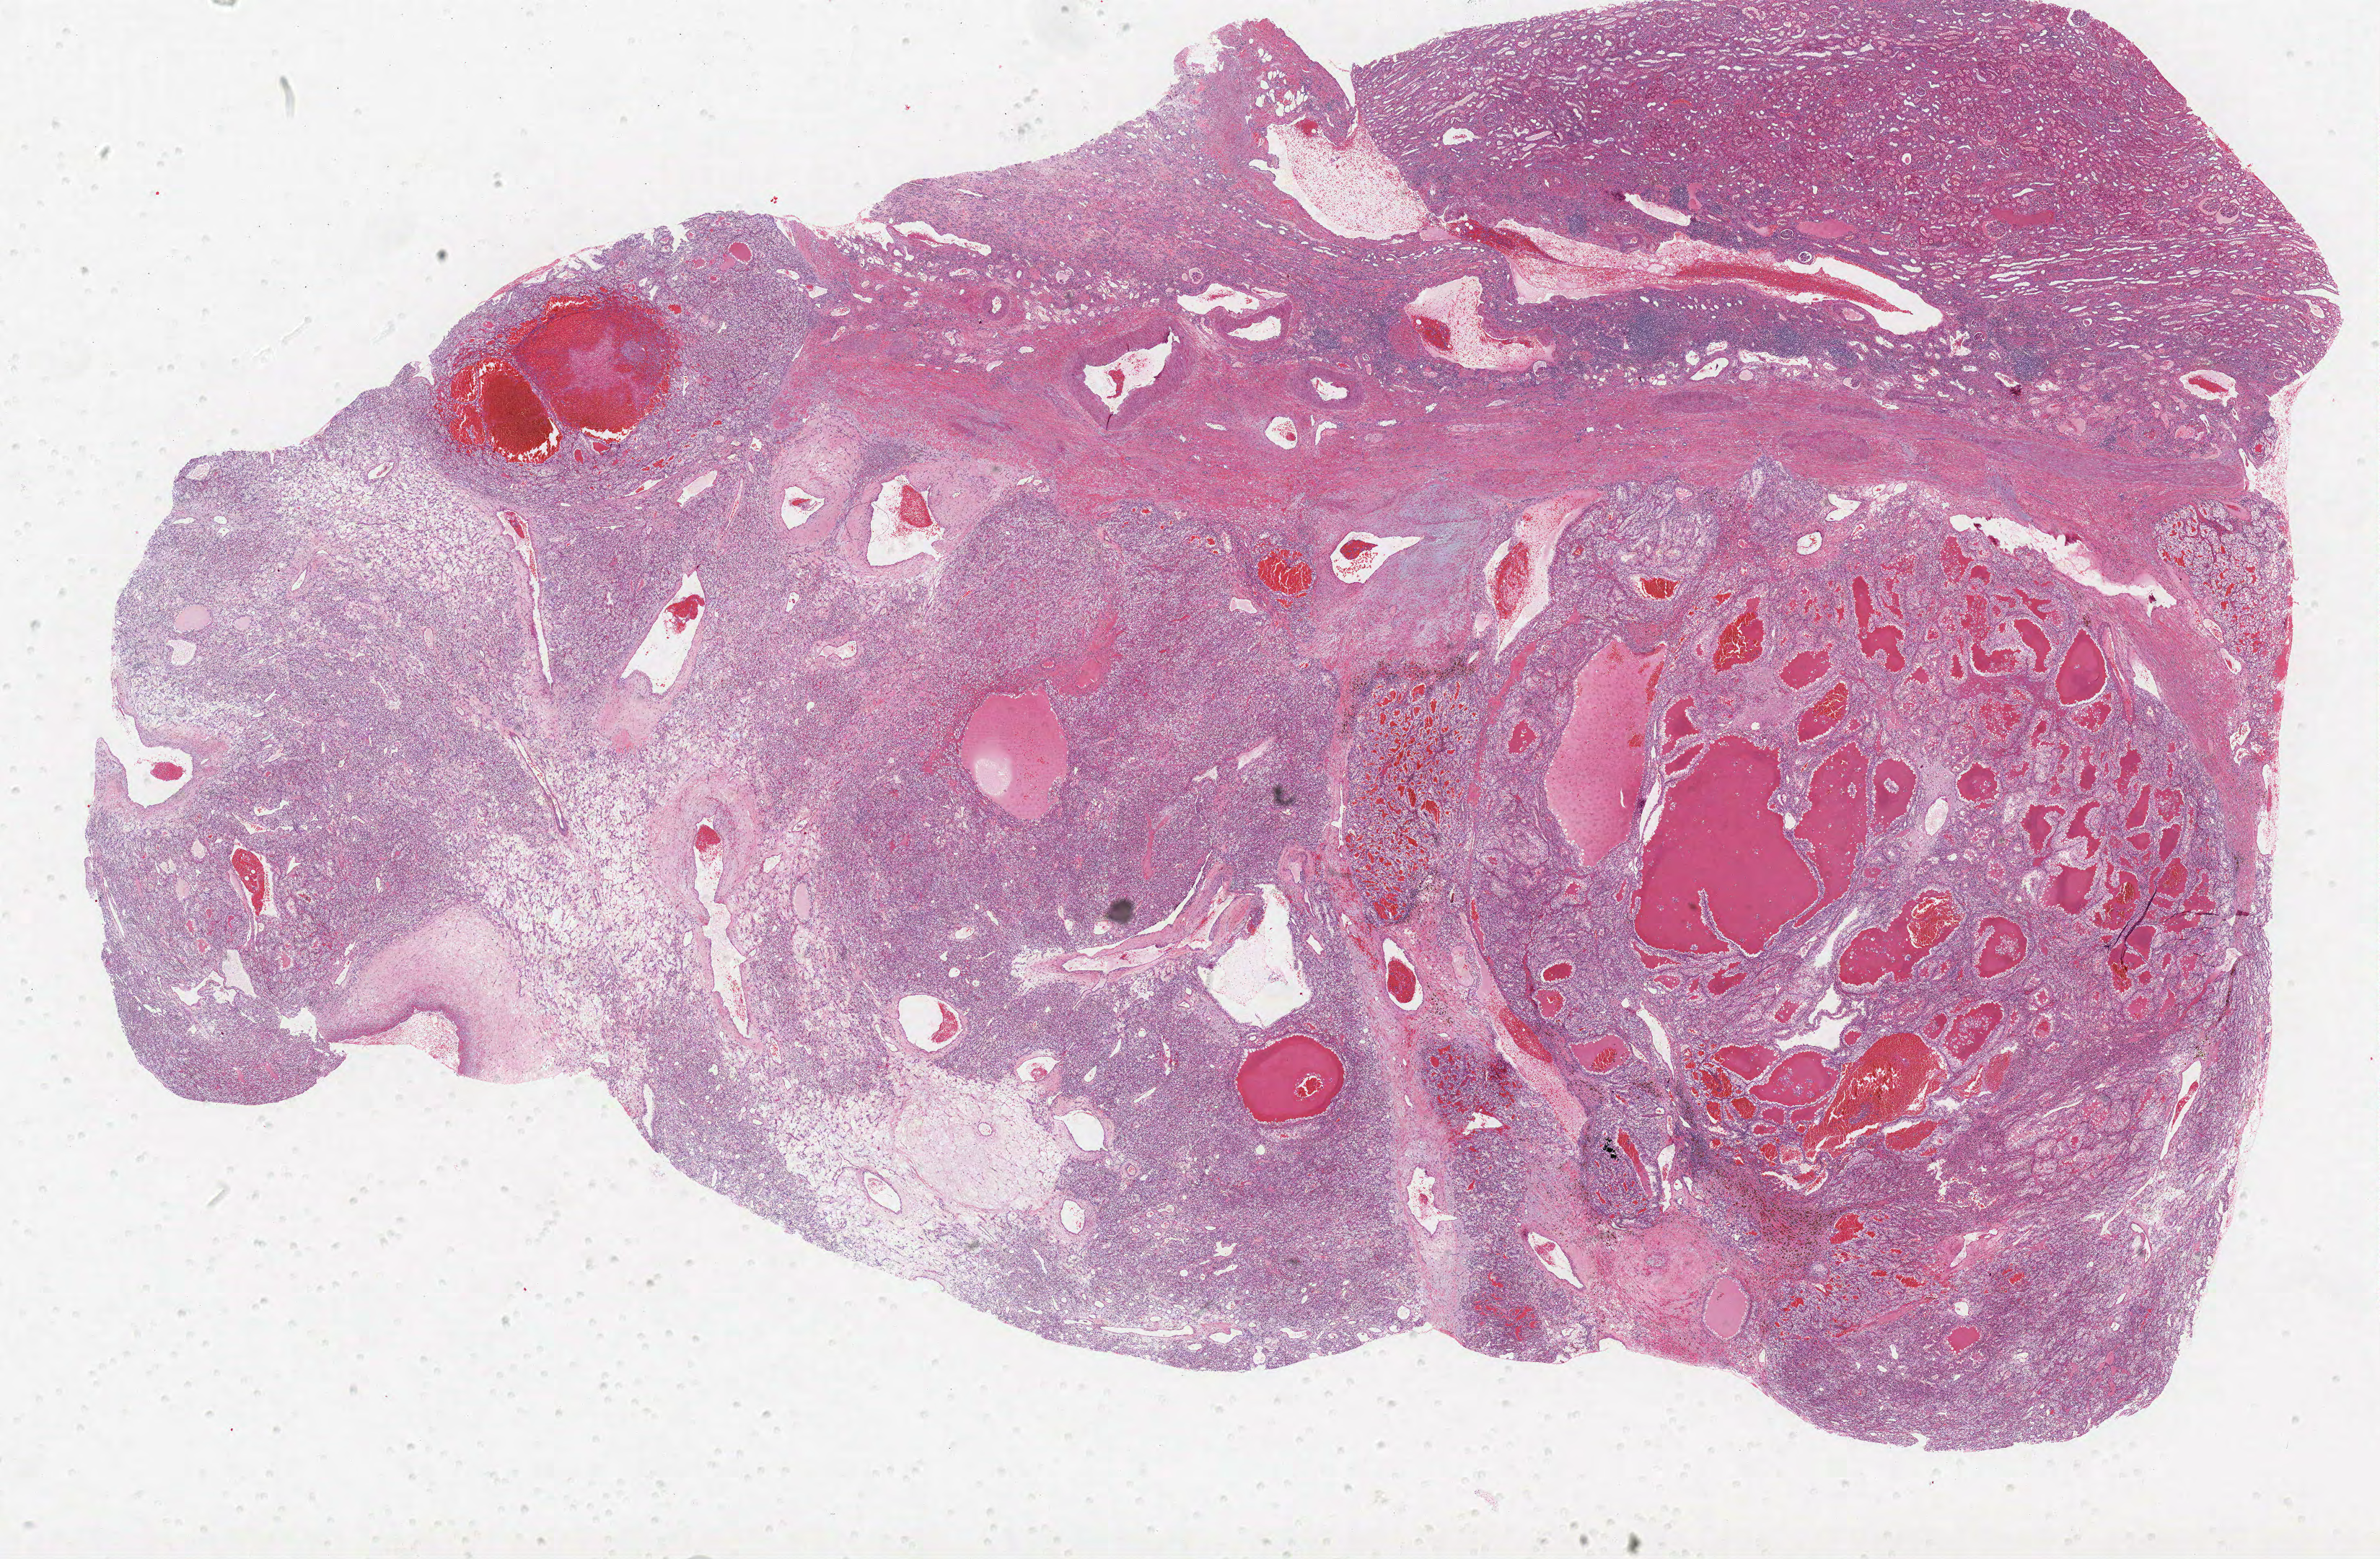
Whole-slide histology image, H&E-stained — low-resolution overview of the scanned area, about 26.4 x 17.3 mm (from a 40x scan); formalin-fixed paraffin-embedded (FFPE) diagnostic section; sample: primary tumour, kidney. Male patient; age at initial diagnosis 46 years. Histologic grade: G3 (poorly differentiated).
- lymph nodes positive (case pathology): 0 of 9 examined
- laterality: left
- pathologic diagnosis: Clear cell adenocarcinoma, NOS
- AJCC pathologic stage: II
- TNM: T2 N0 M0